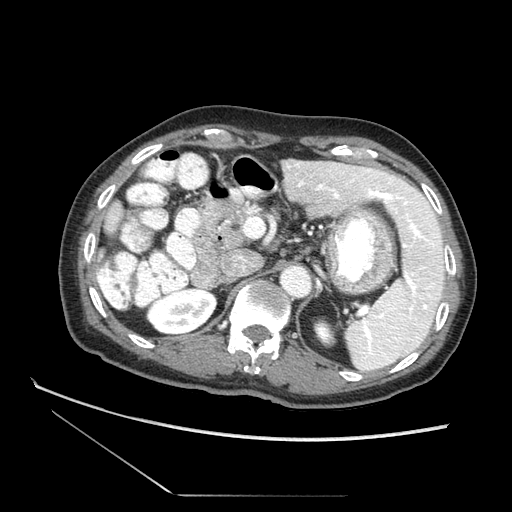
Contrast-enhanced abdominal CT (liver protocol), one axial slice; position 45 of 73 along the scan axis; soft-tissue window (W 400 / L 40 HU); 512 × 512 image matrix, field of view 360 × 360 mm. From the clinical record (not read from this slice): diagnosis: hepatocellular carcinoma (patient treated with transarterial chemoembolisation; whether this scan precedes or follows treatment is not stated here); TNM stage (as recorded): Stage-II; Child-Pugh class: A; tumour differentiation: moderately differentiated.
Structures marked on this image (semi-automatically segmented with operator editing):
- liver parenchyma outside the tumour (the mass and vessels are separate outlines, so this box may not span the whole liver): bounding box <112,158,447,346> (left, top, right, bottom; pixels)
- liver vessels: <299,181,428,306>